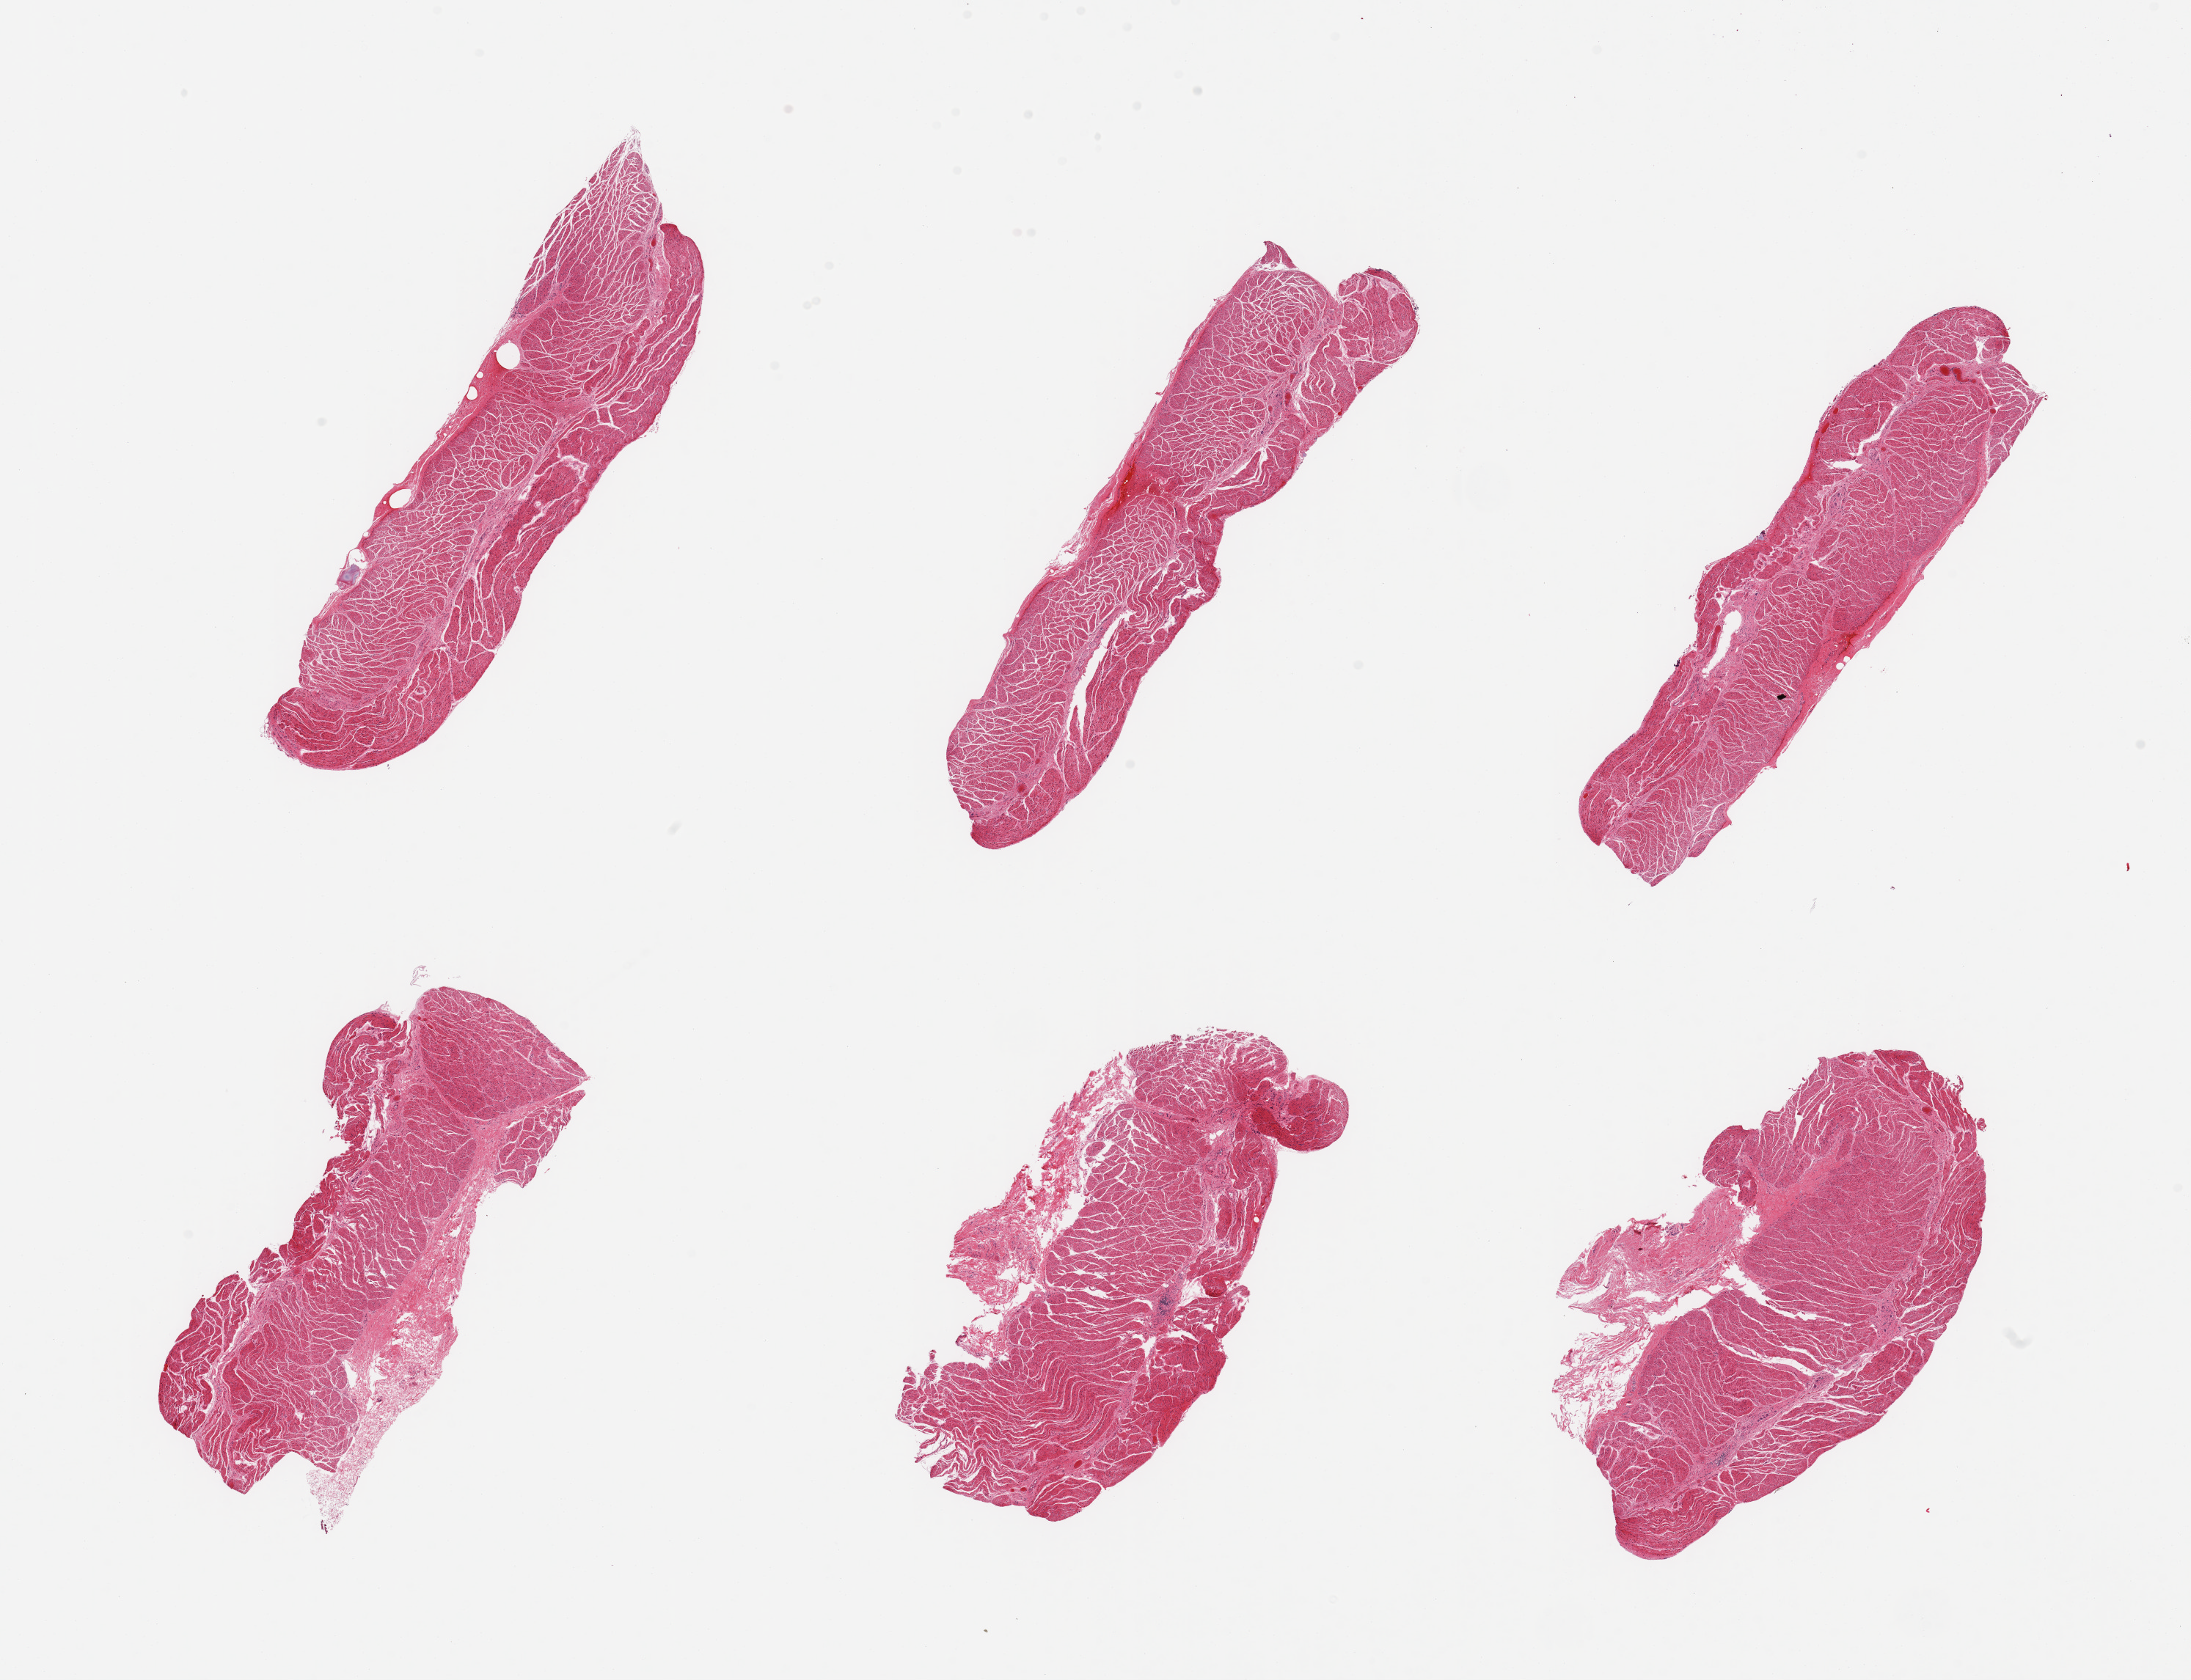
H&E whole-slide image, brightfield — whole scanned area (about 23.6 x 18.1 mm, slide scanned at 20x) shown as a low-resolution overview; PAXgene-fixed, paraffin-embedded tissue; sampled site (target tissue): esophageal muscle; tissue donor sample. Donor sex: male.
Reviewer comment on this tissue sample: 6 pieces; target muscularis; 3 pieces with attached residual loose fibrous tissue.